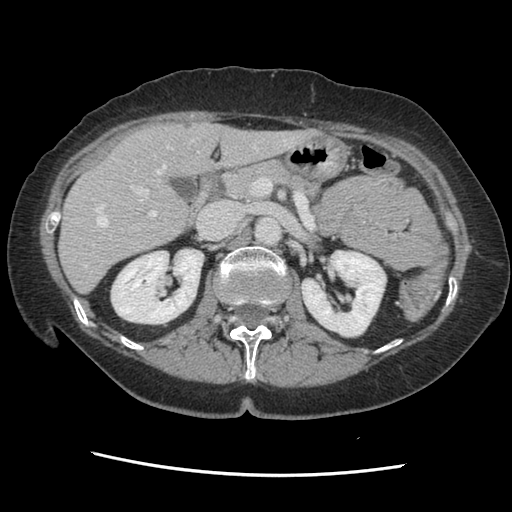
Contrast-enhanced abdominal CT, one axial slice; slice 75 of 141 in the series (ordered by position); soft-tissue window (W 400 / L 40 HU); 2.5 mm slice thickness; 512 × 512 image matrix, field of view 330 × 330 mm. Female patient, age 61 years. From the clinical record (not read from this slice): diagnosis: colorectal cancer liver metastases, imaged before liver resection; multiple liver metastases: no; largest metastasis: 2.4 cm; disease in both lobes: no.
Outlined on this slice (manually delineated by an expert):
- hepatic veins: bounding box <85,144,257,267> (left, top, right, bottom; pixels)
- liver: <60,123,310,292>
- planned liver remnant (the part of the liver to remain after resection): <60,123,309,292>
- portal vein (with intrahepatic branches): <93,185,156,245>
- liver metastasis: <184,122,192,130>